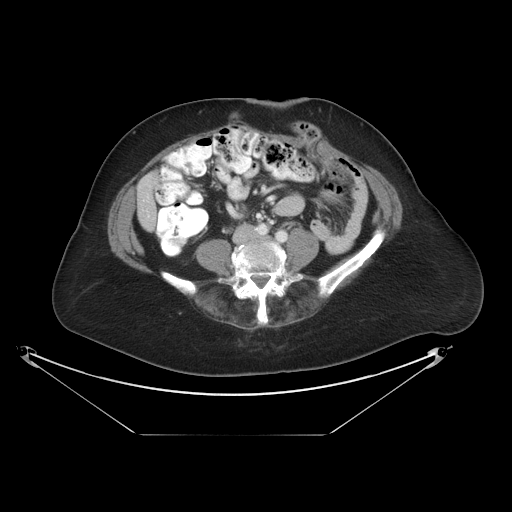
Contrast-enhanced abdominal CT, one axial slice. Position 1 of 36 along the scan axis. Intravenous contrast given. Soft-tissue window (W 400 / L 40 HU). 5 mm slice thickness. 512 × 512 image matrix. Female patient, age 70 years. From the clinical record (not read from this slice): diagnosis: colorectal cancer liver metastases, imaged before liver resection; multiple liver metastases: no; largest metastasis: 2.5 cm; disease in both lobes: no.
Annotated regions visible in this slice (expert manual segmentation):
- liver: bounding box (x1, y1, x2, y2) in pixels: (138, 176, 158, 231)